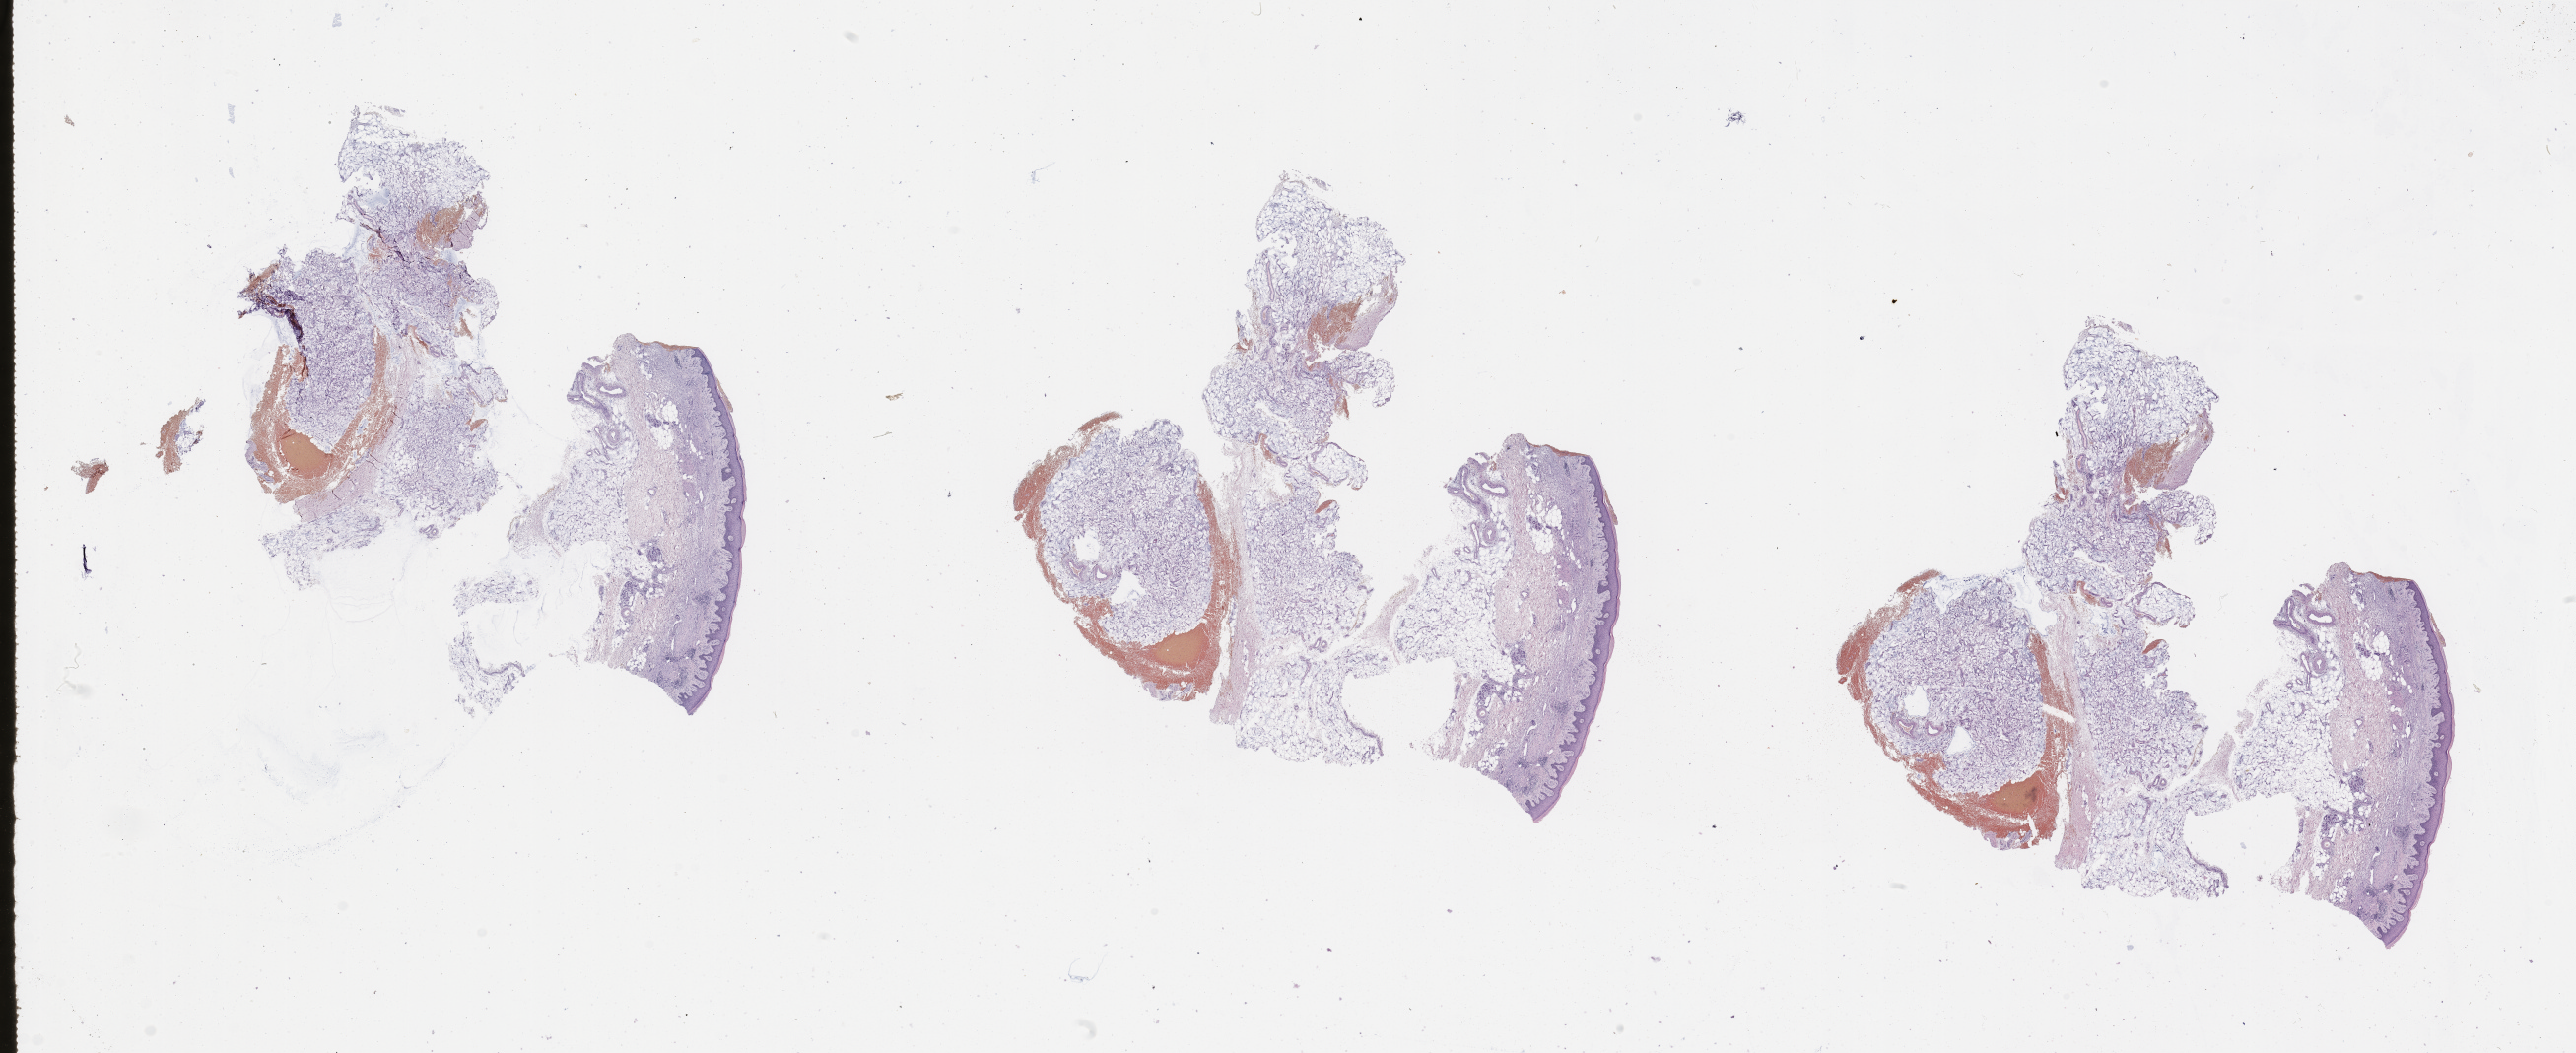
Whole-slide histology image, H&E-stained — whole scanned area (about 41.3 x 16.9 mm, from a 20x scan) shown as a low-resolution overview, normal (non-tumour) tissue sample, sampled site: skin. Female patient, aged 90 or older.
- this section: normal (non-tumour) tissue from the same patient
- patient diagnosis: Malignant melanoma, NOS